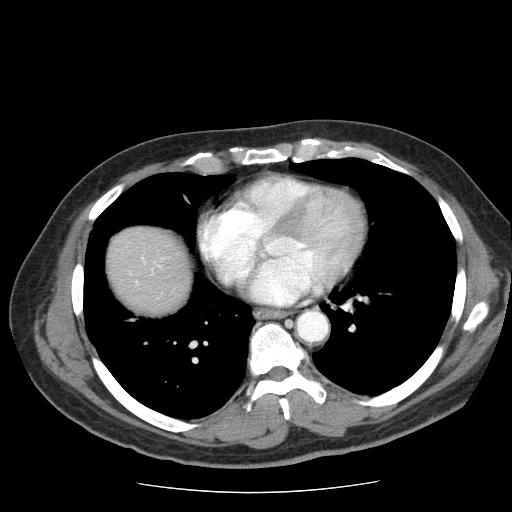
Contrast-enhanced abdominal CT (liver protocol), one axial slice. Slice 74 of 85 in the series (ordered by position). Reconstruction kernel STANDARD. 120 kVp. Soft-tissue window (W 400 / L 40 HU). 512 × 512 image matrix, field of view 360 × 360 mm. From the clinical record (not read from this slice): diagnosis: hepatocellular carcinoma (patient treated with transarterial chemoembolisation; whether this scan precedes or follows treatment is not stated here); TNM stage (as recorded): Stage-IIIA.
Annotated regions visible in this slice (semi-automatic segmentation, software-assisted and operator-edited):
- liver parenchyma outside the tumour (the mass and vessels are separate outlines, so this box may not span the whole liver): bounding box [x1, y1, x2, y2] px = [108, 226, 190, 312]